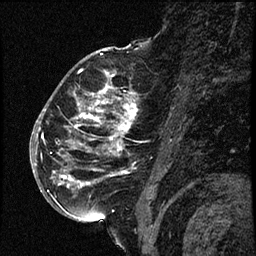
Breast MRI (dynamic contrast-enhanced), one sagittal slice; slice 38 of 66 in the series (ordered by position); dynamic contrast-enhanced study with each time point stored as its own series, time point 2 of 3 at this slice position (early post-contrast, ordered by acquisition time); 1.5 T; TE 4.2 ms, TR 17.6 ms; 256 × 256 image matrix, field of view 200 × 200 mm. Female patient. Case-level facts recorded for this patient, not image findings: setting: breast cancer imaged before/during neoadjuvant chemotherapy; receptor status: HER2-positive.
Annotated regions visible in this slice (semi-automatically segmented with operator editing):
- analysis volume of interest (the breast-tissue region the enhancement analysis was run in; not a lesion): bounding box <52,69,147,209> (left, top, right, bottom; pixels)
- tumour enhancement mask (voxels above the 100 % enhancement threshold inside the analysis volume of interest): <59,76,137,187>